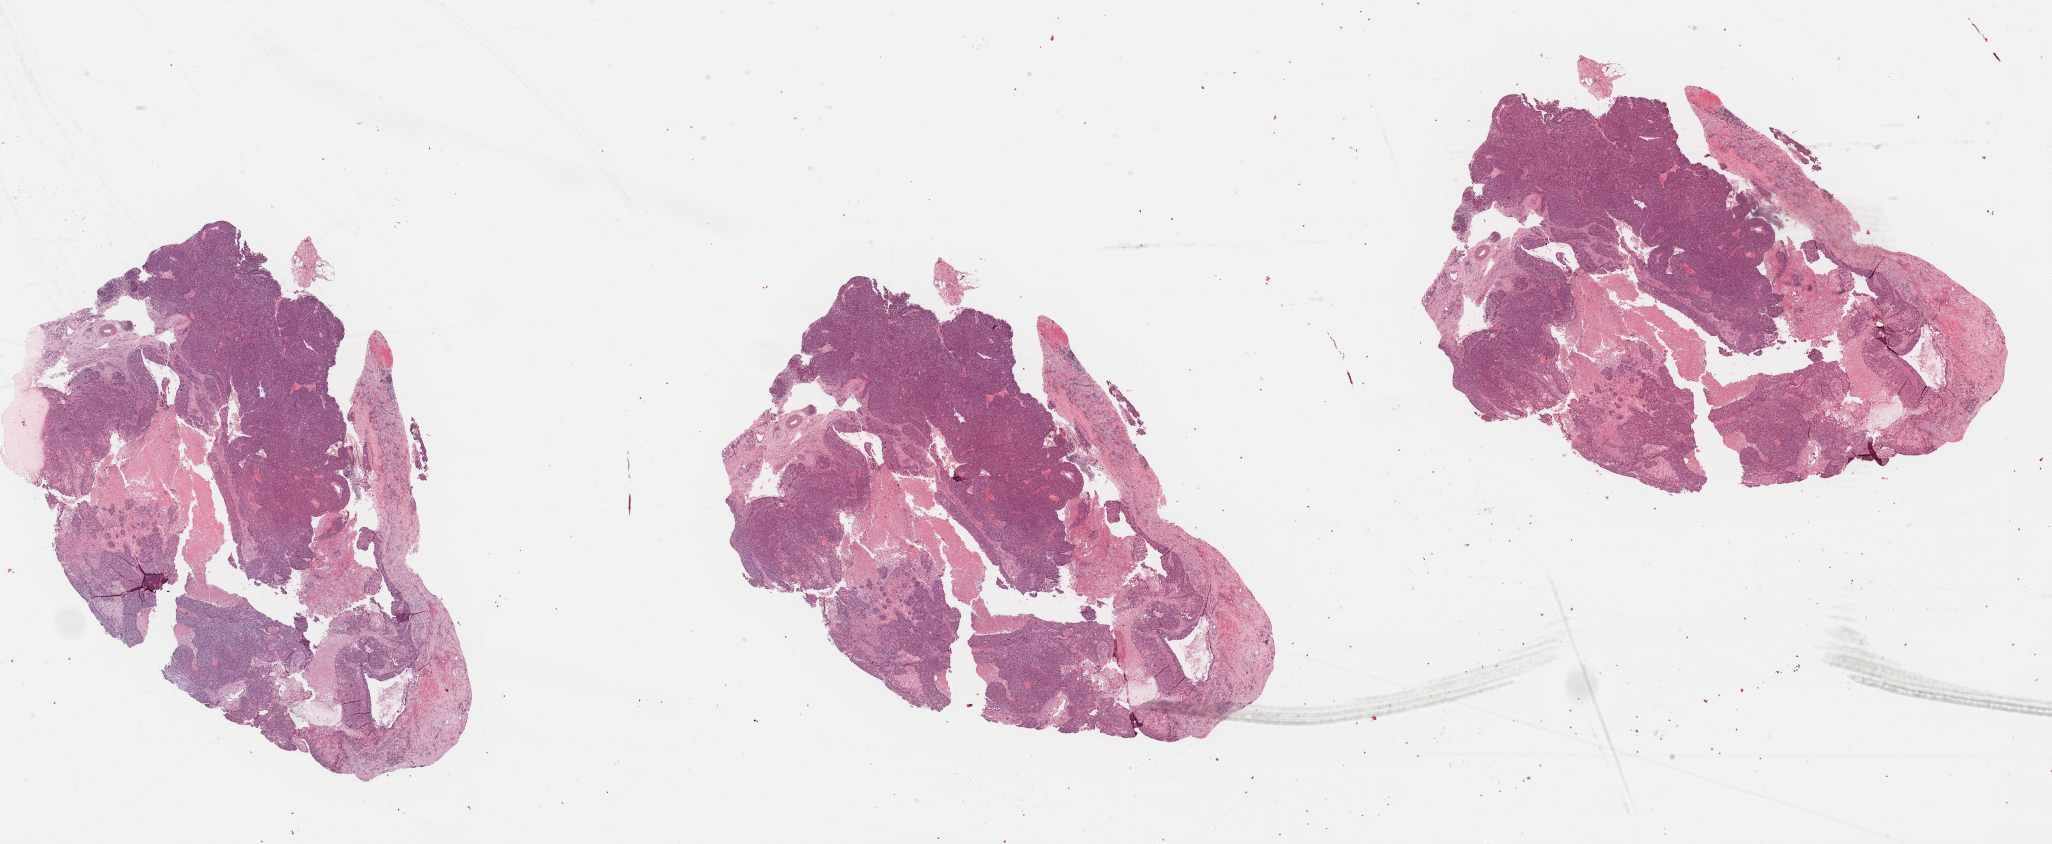
Whole-slide histology image, H&E — shown as a low-resolution overview of the whole scanned area (about 32.4 x 13.3 mm, slide scanned at 40x), FFPE section, breast, primary tumour sample. Patient: female, age at initial diagnosis 57 years.
* laterality: left
* histologic diagnosis: Infiltrating duct carcinoma, NOS
* AJCC pathologic stage: IIA
* lymph nodes positive (case pathology): 0 of 1 examined